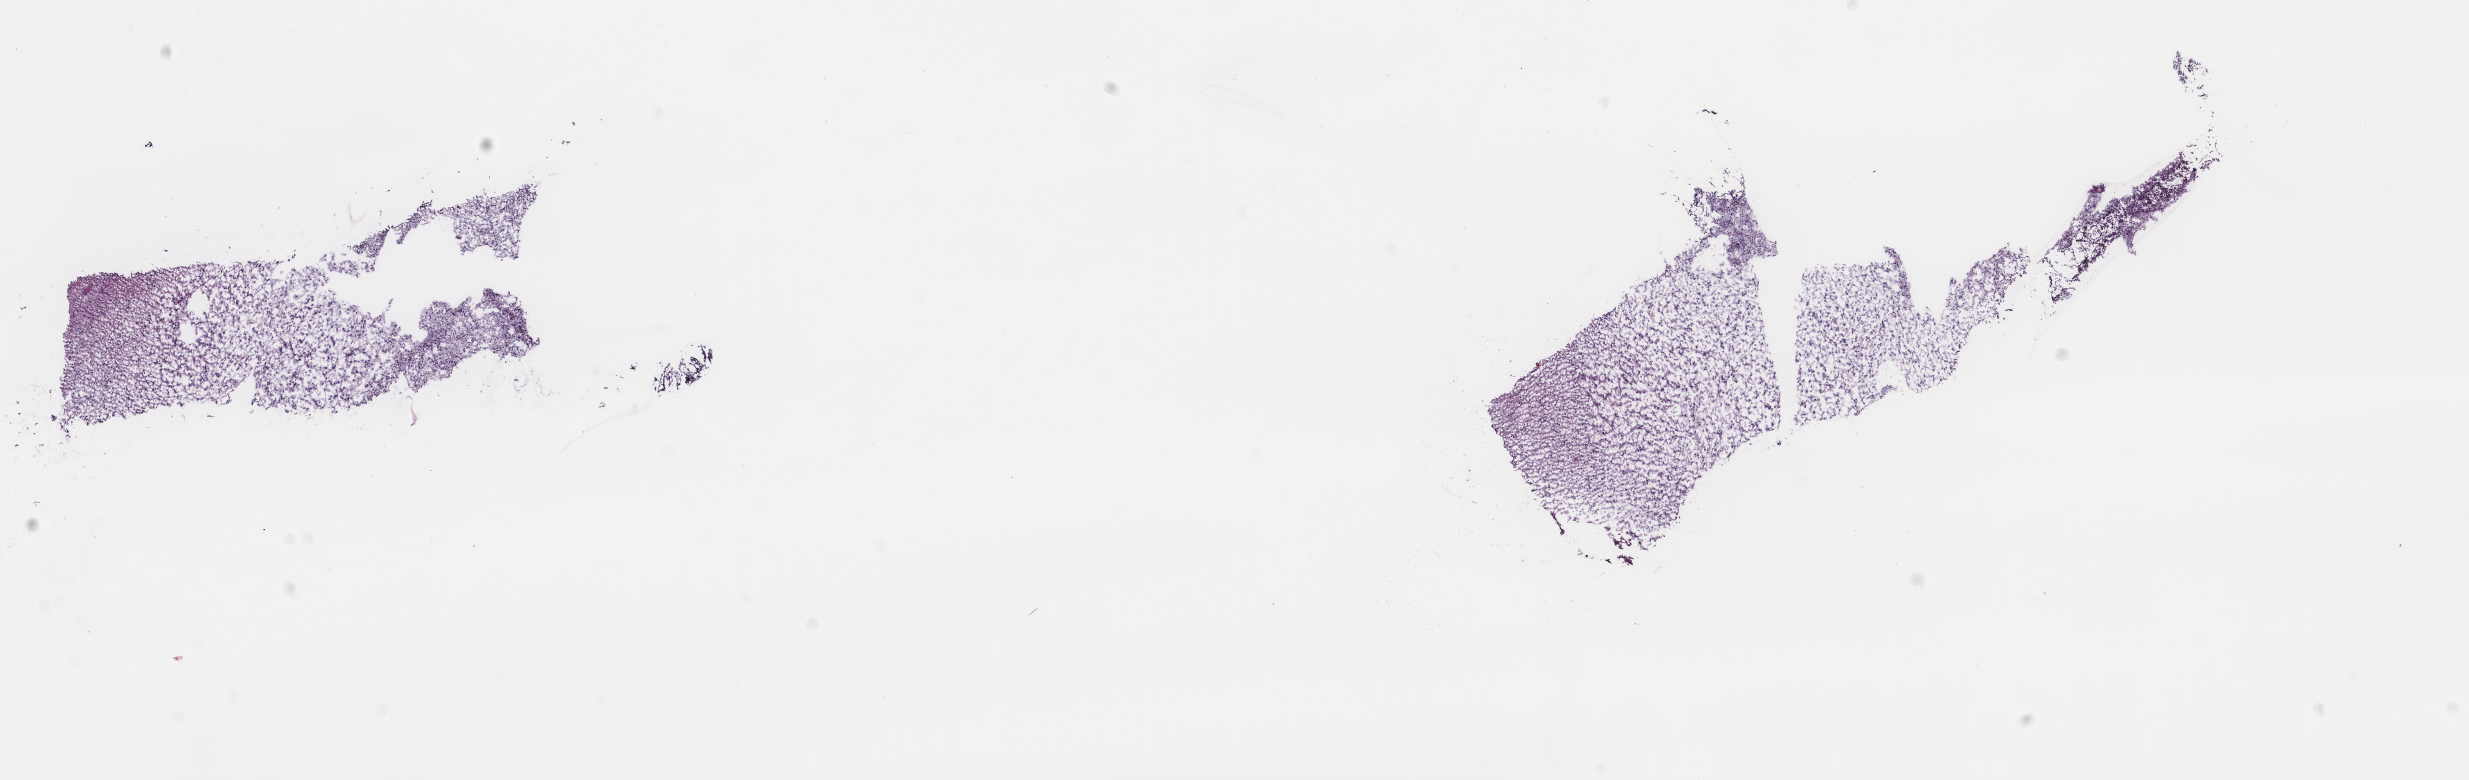
Digitized H&E tissue section (whole slide) — a low-resolution overview of the entire scanned area, about 19.6 x 6.2 mm (slide scanned at 40x), frozen section from the top of the tissue portion, brain, primary tumour sample. Male patient; age at initial diagnosis 32 years. Histologic grade: G3 (poorly differentiated). Composition of this section per pathologist review: tumour cells 60%, tumour nuclei 85%, normal cells 35%, stromal cells 5%, necrosis 0%. Inflammatory infiltration, as recorded: lymphocyte infiltration 0%, monocyte infiltration 0%, neutrophil infiltration 0%.
• pathologic diagnosis: Astrocytoma, anaplastic (temporal lobe)
• laterality: right